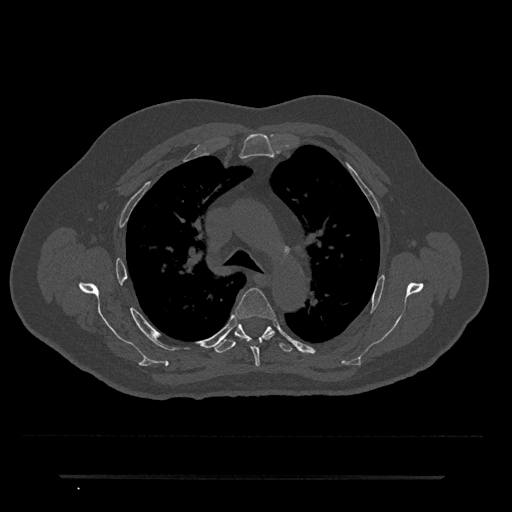
CT including the spine, one axial slice. Position 508 of 797 along the scan axis. 120 kVp. Bone window (W 1800 / L 400 HU). 0.5 mm slice thickness. 512 × 512 image matrix, field of view 437 × 437 mm. Male patient, age 69 years. From the clinical record (not read from this slice): primary cancer: prostate.
Structures marked on this image (semi-automatically segmented with operator editing):
- T4 vertebra: bounding box (x1, y1, x2, y2) in pixels: (234, 288, 276, 367)
- T5 vertebra: (212, 320, 292, 353)